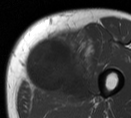
MRI of an extremity soft-tissue mass, one axial slice. Position 21 of 55 along the scan axis. MR volume resampled by the dataset authors to the PET/CT grid (not the native acquisition matrix). 3.27 mm slice thickness. 131 × 118 image matrix. Male patient. From the clinical record (not read from this slice): histological type: pleiomorphic liposarcoma; grade: high; site of the primary tumour: left thigh.
Structures marked on this image (expert contour drawn on MRI and transferred to this co-registered scan by the dataset authors):
- gross tumour volume including surrounding oedema: bounding box [x1, y1, x2, y2] px = [25, 32, 97, 104]
- gross tumour volume (mass): [25, 36, 90, 97]